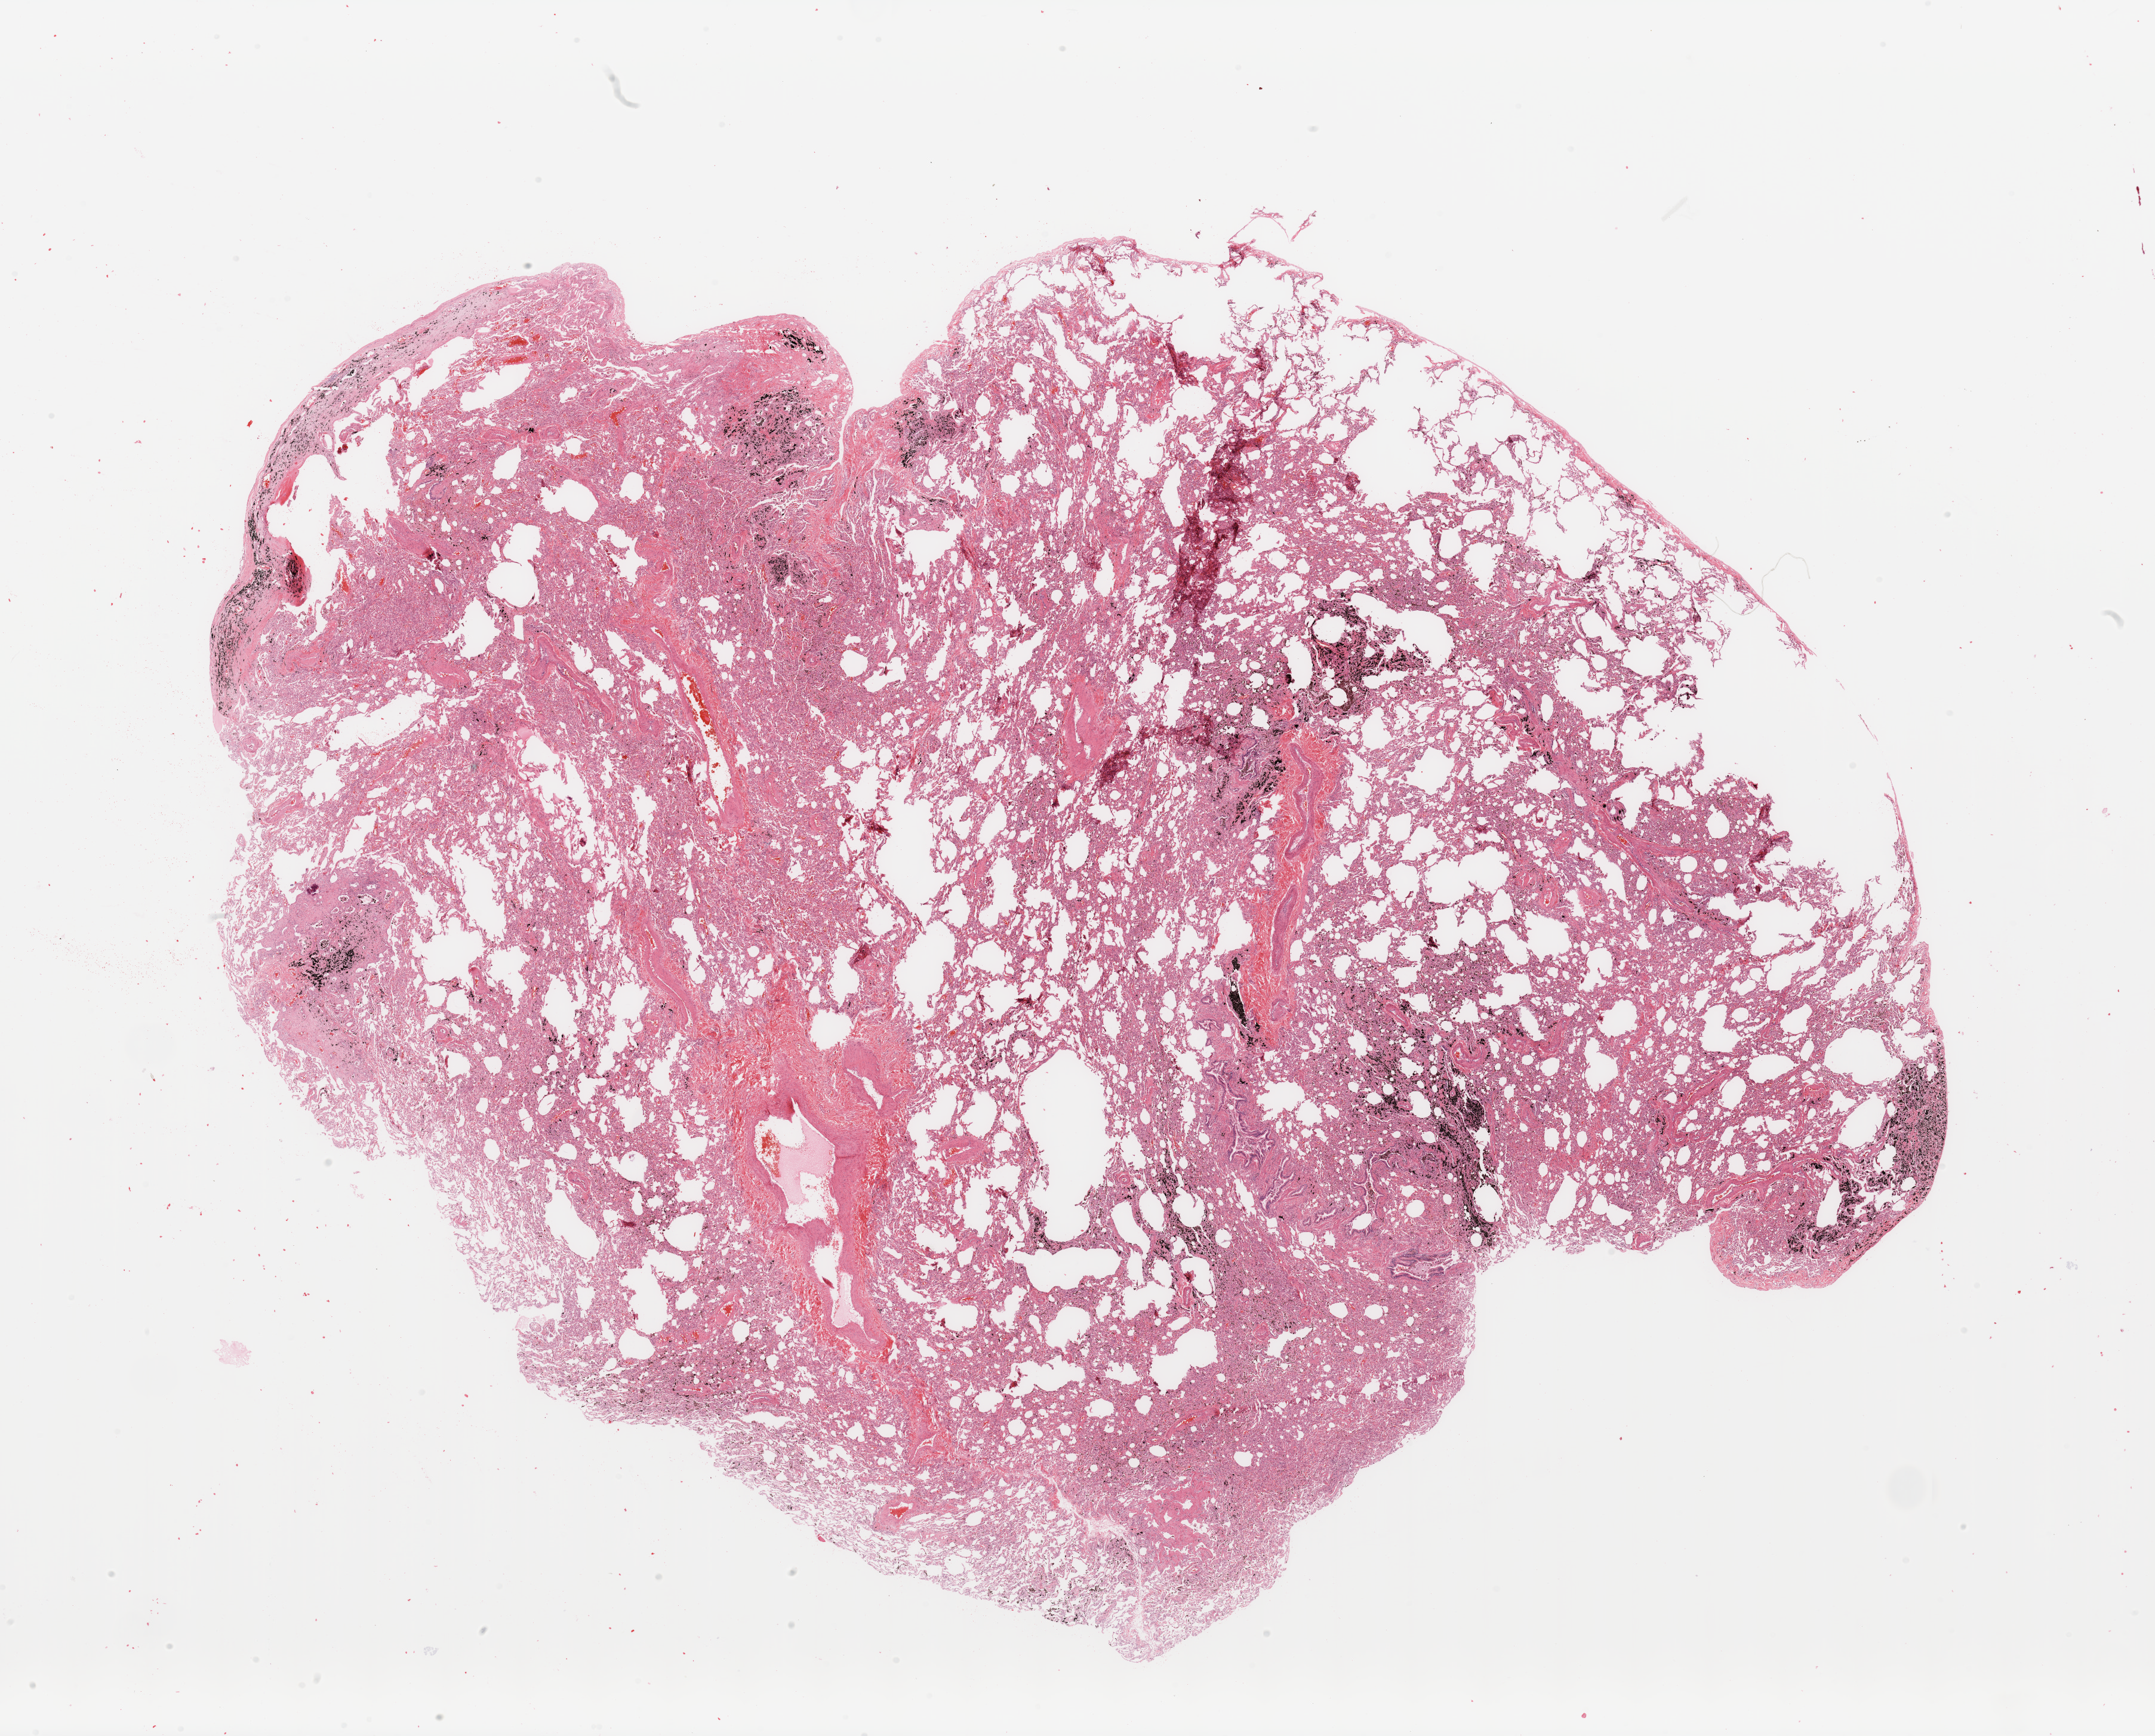
Digitized Hematoxylin and eosin (H&E) stained tissue section (whole slide) — whole scanned area (about 28.5 x 23.0 mm) shown as a low-resolution overview; normal (non-tumour) tissue sample, sampled site: lung. Patient: male, age 58 years.
* this section: normal (non-tumour) tissue from the same patient
* patient diagnosis: Adenocarcinoma, NOS